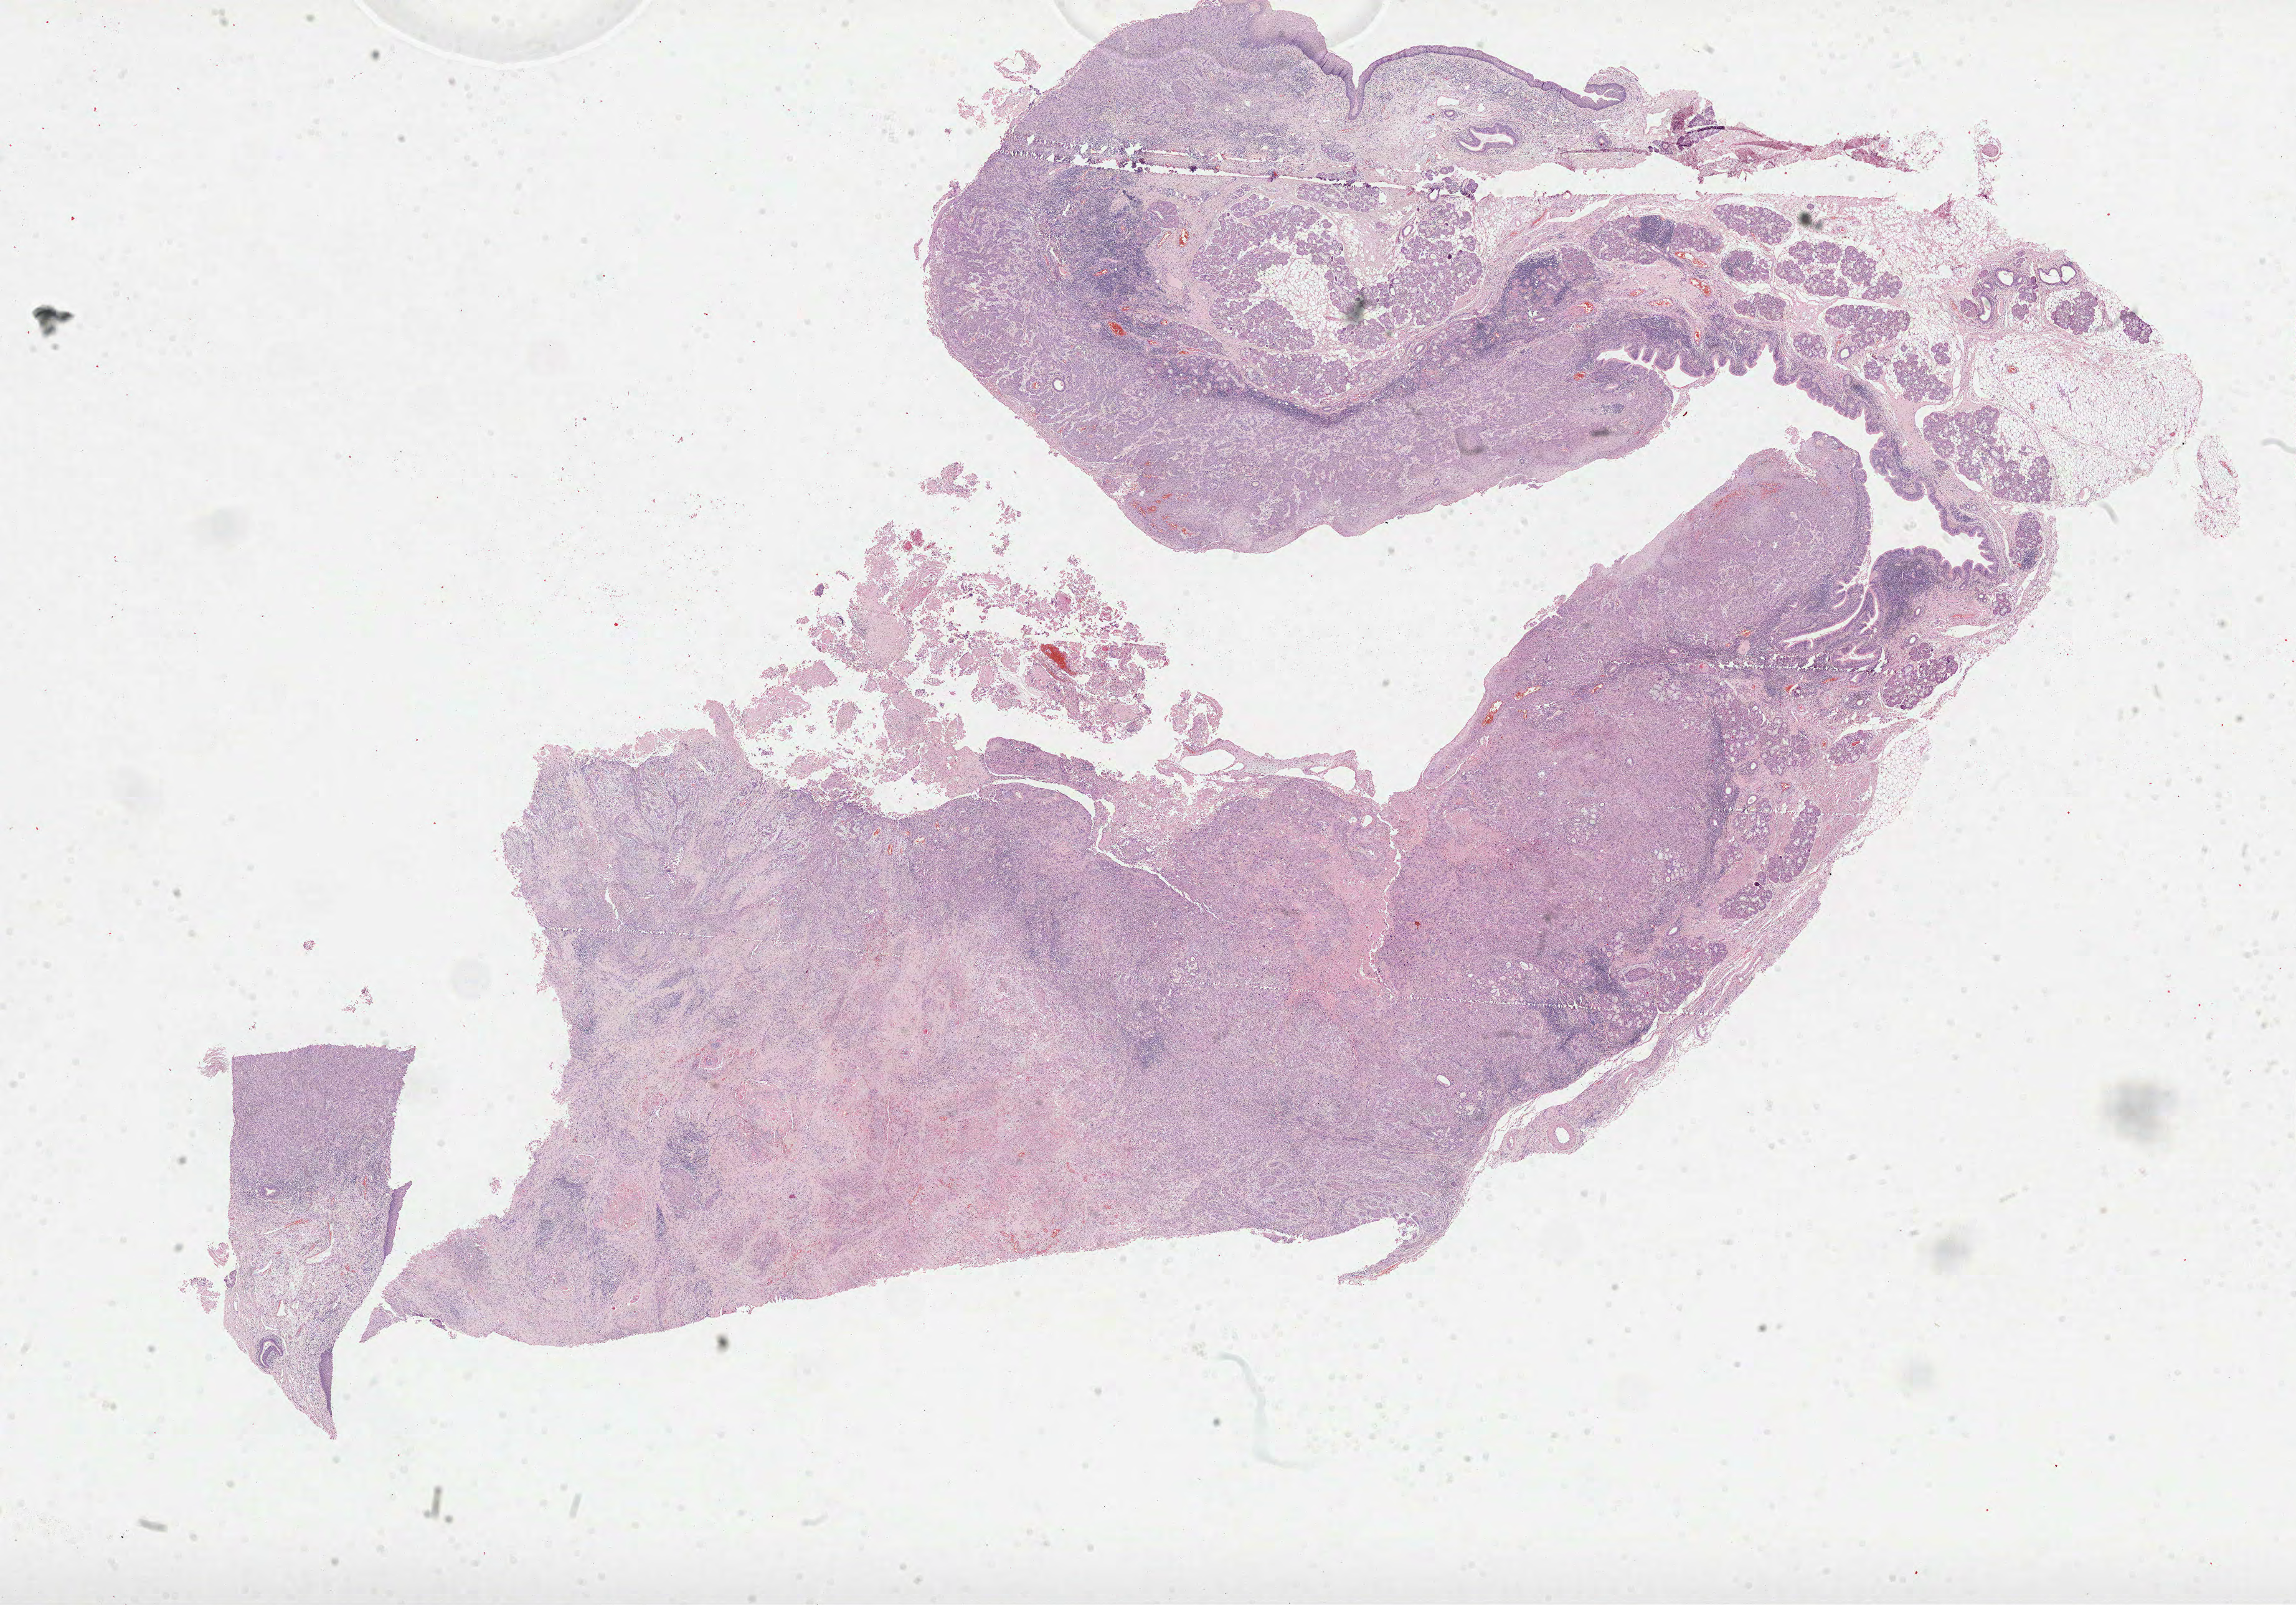
Whole-slide histology image, H&E-stained, a low-resolution overview of the entire scanned area, about 29.7 x 20.8 mm (slide scanned at 40x), formalin-fixed paraffin-embedded (FFPE) diagnostic section, primary tumour sample from the head and neck. Male patient; age at initial diagnosis 59 years. Histologic grade: G2 (moderately differentiated).
TNM: T3 N0. Pathologic diagnosis: Squamous cell carcinoma, NOS. AJCC pathologic stage: III (7th edition).